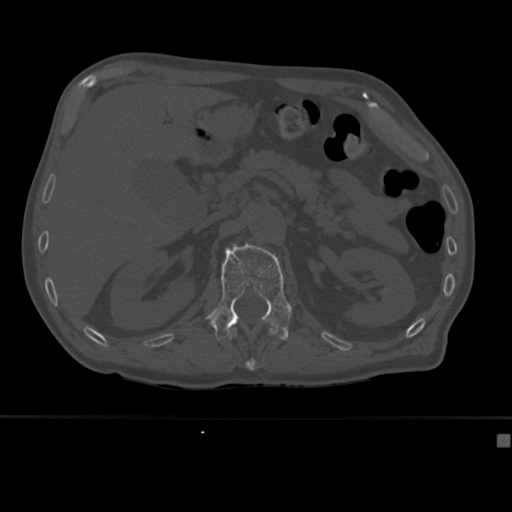
CT including the spine, one axial slice. Position 174 of 430 along the scan axis. Bone window (W 1800 / L 400 HU). 512 × 512 image matrix, field of view 337 × 337 mm. Patient: male, 64 years. From the clinical record (not read from this slice): primary cancer: uterus; vertebrae with lytic lesions (as recorded): T1, T4, T5, T7, L5.
Outlined on this slice (semi-automatic segmentation, software-assisted and operator-edited):
- L1 vertebra: box from (x=207, y=243) to (x=292, y=341) px
- T12 vertebra: (x=229, y=327)–(x=275, y=371)